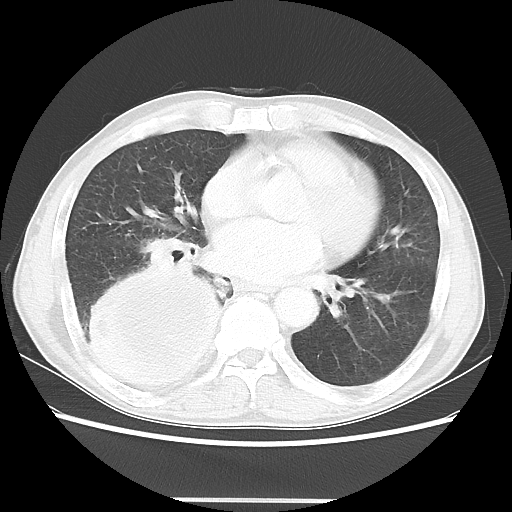
Chest CT, one axial slice; reconstruction kernel LUNG; 100 kVp; lung window (W 1500 / L -600 HU); 512 × 512 image matrix, field of view 361 × 361 mm. Patient: male, 66 years. From the clinical record (not read from this slice): clinical TNM (as recorded): T4 N1 M1.
Annotated regions visible in this slice (bounding box drawn by a radiologist):
- lung tumour (recorded histology: small cell carcinoma): box from (x=78, y=250) to (x=245, y=405) px